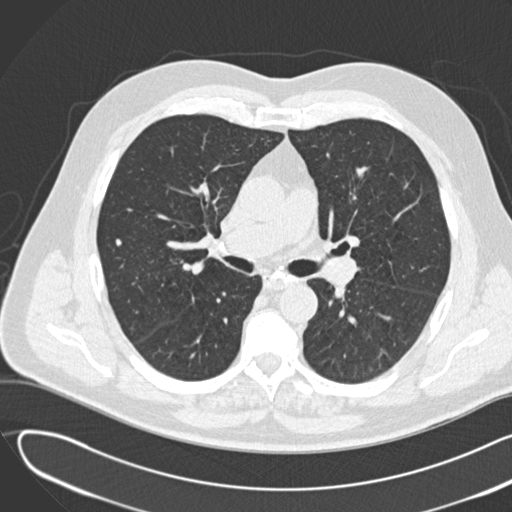
Low-dose screening chest CT, one axial slice. Position 83 of 155 along the scan axis. Reconstruction kernel B30f. Lung window (W 1500 / L -600 HU). 2 mm slice thickness. 512 × 512 image matrix, field of view 380 × 380 mm.
Outlined on this slice (expert manual segmentation):
- lesion 1 (tumor, lower lobe of right lung): bounding box (x1, y1, x2, y2) in pixels: (116, 238, 122, 246)